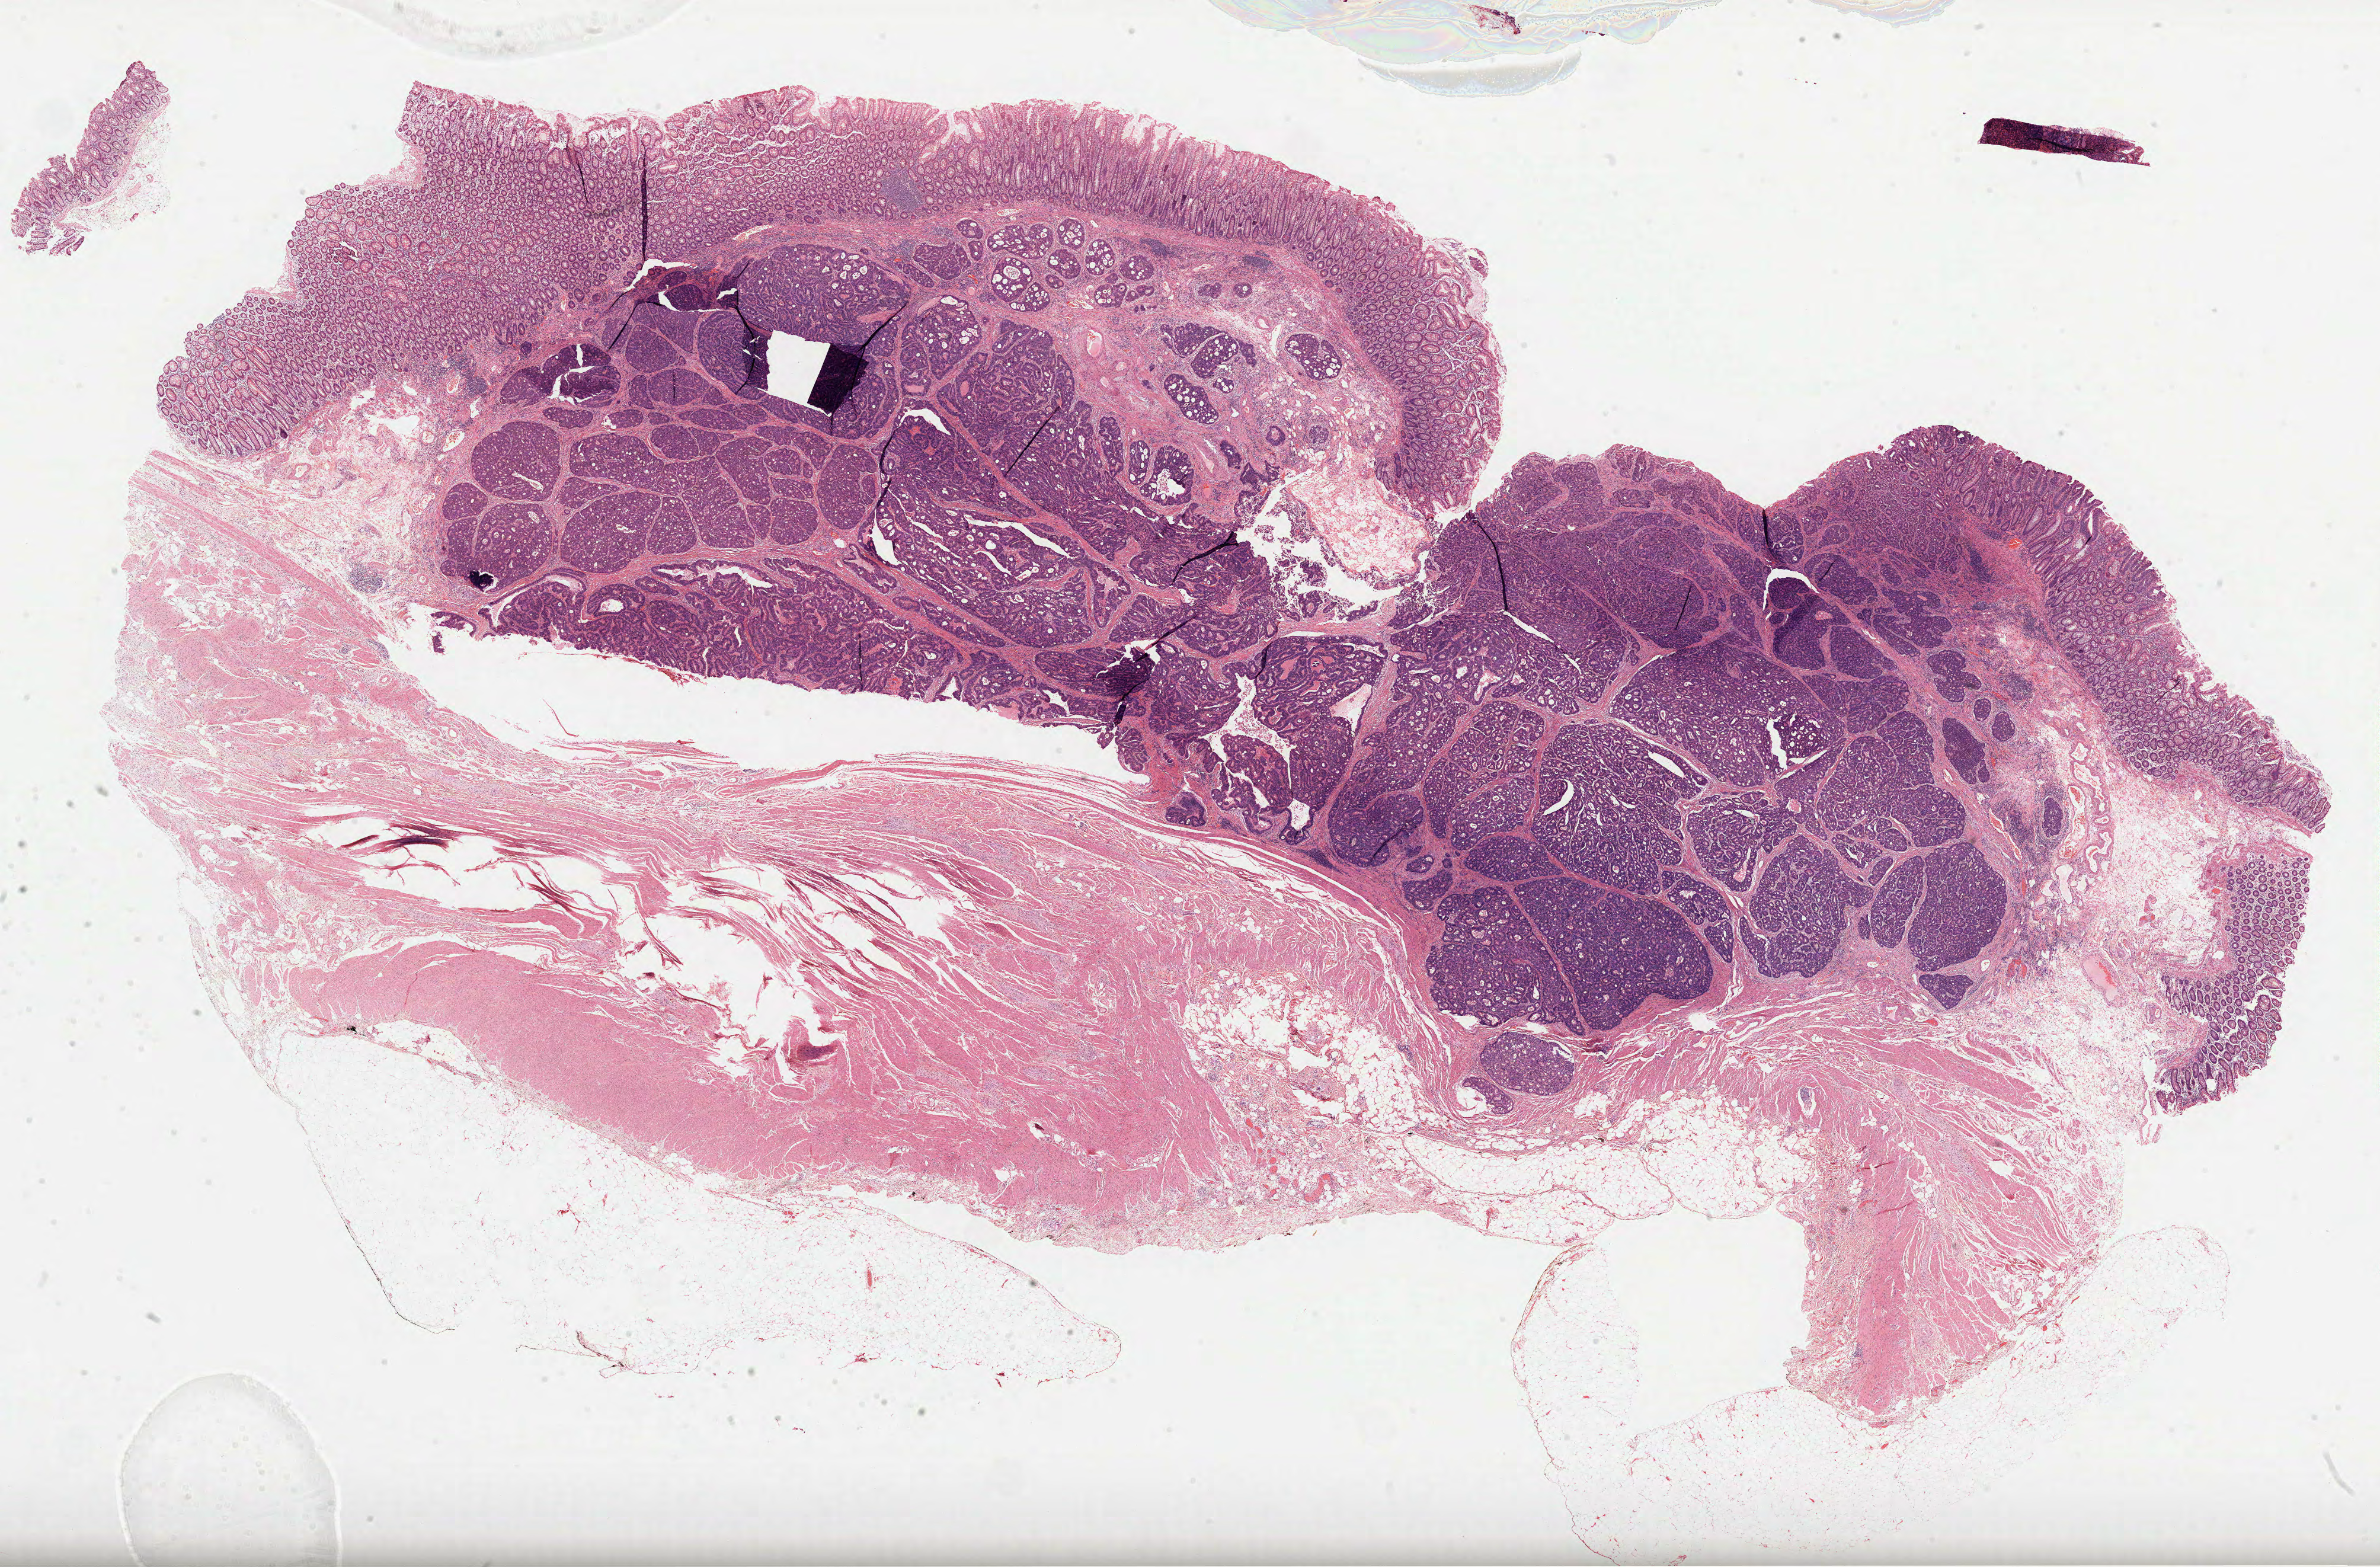
H&E whole-slide image, low-resolution overview of the scanned area, about 32.4 x 21.3 mm. Formalin-fixed paraffin-embedded (FFPE) diagnostic section. Sample: primary tumour, colon. Male patient; age at initial diagnosis 81 years.
Histologic diagnosis: Adenocarcinoma, NOS (ascending colon). AJCC pathologic stage: I. TNM: T2 N0 MX.